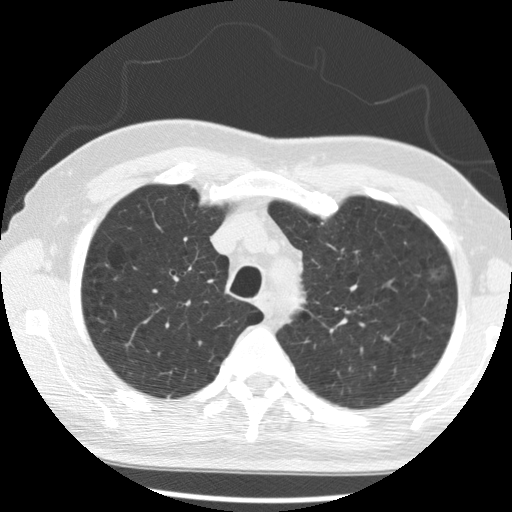
Axial slice from a low-dose chest CT screening exam; second screening round (one year after baseline); lung window (W 1500 / L -600 HU); 2.5 mm slice thickness; slice 65 of 285 in the series. Male, age 68 years at enrolment.
Expert-annotated lung lesion, bounding box <414,259,460,294> (left, top, right, bottom; pixels). Reader record for this screening exam (exam-level; its link to the box is not recorded): non-calcified nodule or mass ≥4 mm, left upper lobe, 15 × 11 mm, poorly defined margins, ground glass attenuation, pre-existing on the prior screen: yes; interval growth: yes. Lung cancer was diagnosed 278 days after this screen: bronchiolo-alveolar adenocarcinoma, NOS, left upper lobe, moderately differentiated (G2), stage IA (AJCC 6th edition), 17 mm at pathology.